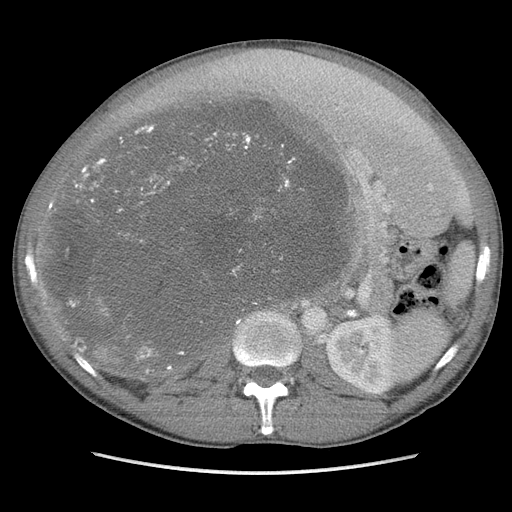
Contrast-enhanced abdominal CT, one axial slice. Position 61 of 115 along the scan axis. Soft-tissue window (W 400 / L 40 HU). 512 × 512 image matrix, field of view 360 × 360 mm. Male patient. Case-level facts recorded for this patient, not image findings: diagnosis: adrenocortical carcinoma; tumour side: right adrenal; Ki-67 index: 13 %; stage (as recorded): 3.
Outlined on this slice (semi-automatic segmentation, software-assisted and operator-edited):
- mass: bounding box (x1, y1, x2, y2) in pixels: (51, 95, 343, 362)